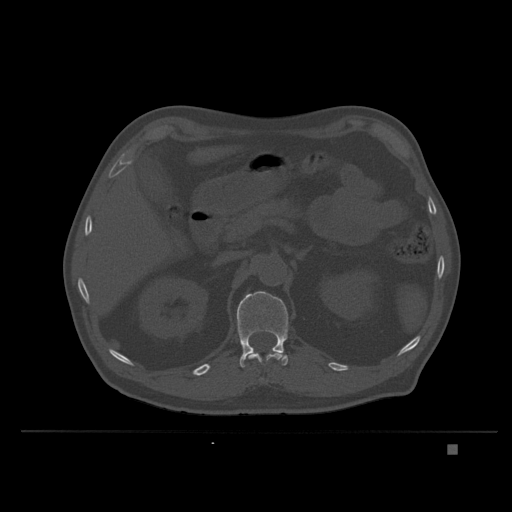
CT including the spine, one axial slice; slice 145 of 435 in the series (ordered by position); bone window (W 1800 / L 400 HU); 1.5 mm slice thickness; 512 × 512 image matrix, field of view 434 × 434 mm. Male patient, age 73 years. Case-level facts recorded for this patient, not image findings: primary cancer: skin.
Outlined on this slice (semi-automatic segmentation, software-assisted and operator-edited):
- L1 vertebra: bounding box [x1, y1, x2, y2] px = [236, 291, 288, 368]
- T12 vertebra: [247, 350, 283, 383]